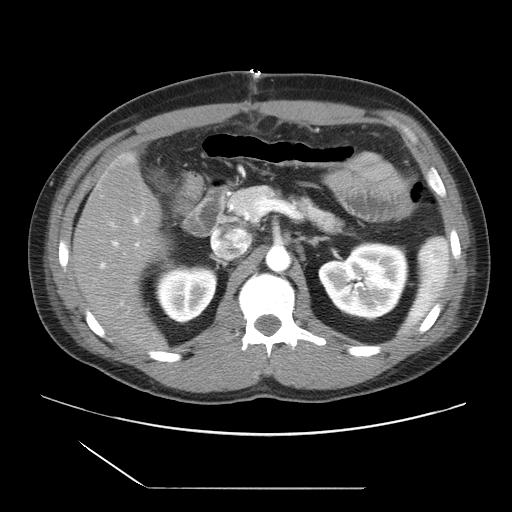
Contrast-enhanced abdominal CT, one axial slice; slice 11 of 39 in the series (ordered by position); 120 kVp; intravenous contrast given; soft-tissue window (W 400 / L 40 HU); 5 mm slice thickness; 512 × 512 image matrix, field of view 395 × 395 mm. Male patient, age 39 years. From the clinical record (not read from this slice): diagnosis: colorectal cancer liver metastases, imaged before liver resection; multiple liver metastases: yes; largest metastasis: 1.3 cm; disease in both lobes: no.
Outlined on this slice (manually delineated by an expert):
- hepatic veins: box from (x=217, y=232) to (x=242, y=258) px
- liver: (x=72, y=154)–(x=166, y=354)
- portal vein (with intrahepatic branches): (x=100, y=215)–(x=142, y=305)